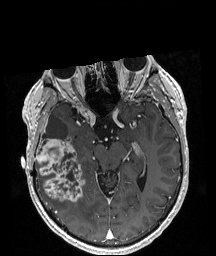
Brain MRI from a brain-tumour surgery series, one axial slice. Slice 120 of 208 in the series (ordered by position). T1-weighted post-contrast. 216 × 256 image matrix, field of view 211 × 250 mm. From the clinical record (not read from this slice): histopathology: Astrocytoma; WHO grade: 4; IDH mutation: yes; tumour location: Right Temporal.
Annotated regions visible in this slice (manually delineated by an expert):
- tumour: bounding box (x1, y1, x2, y2) in pixels: (36, 135, 86, 201)